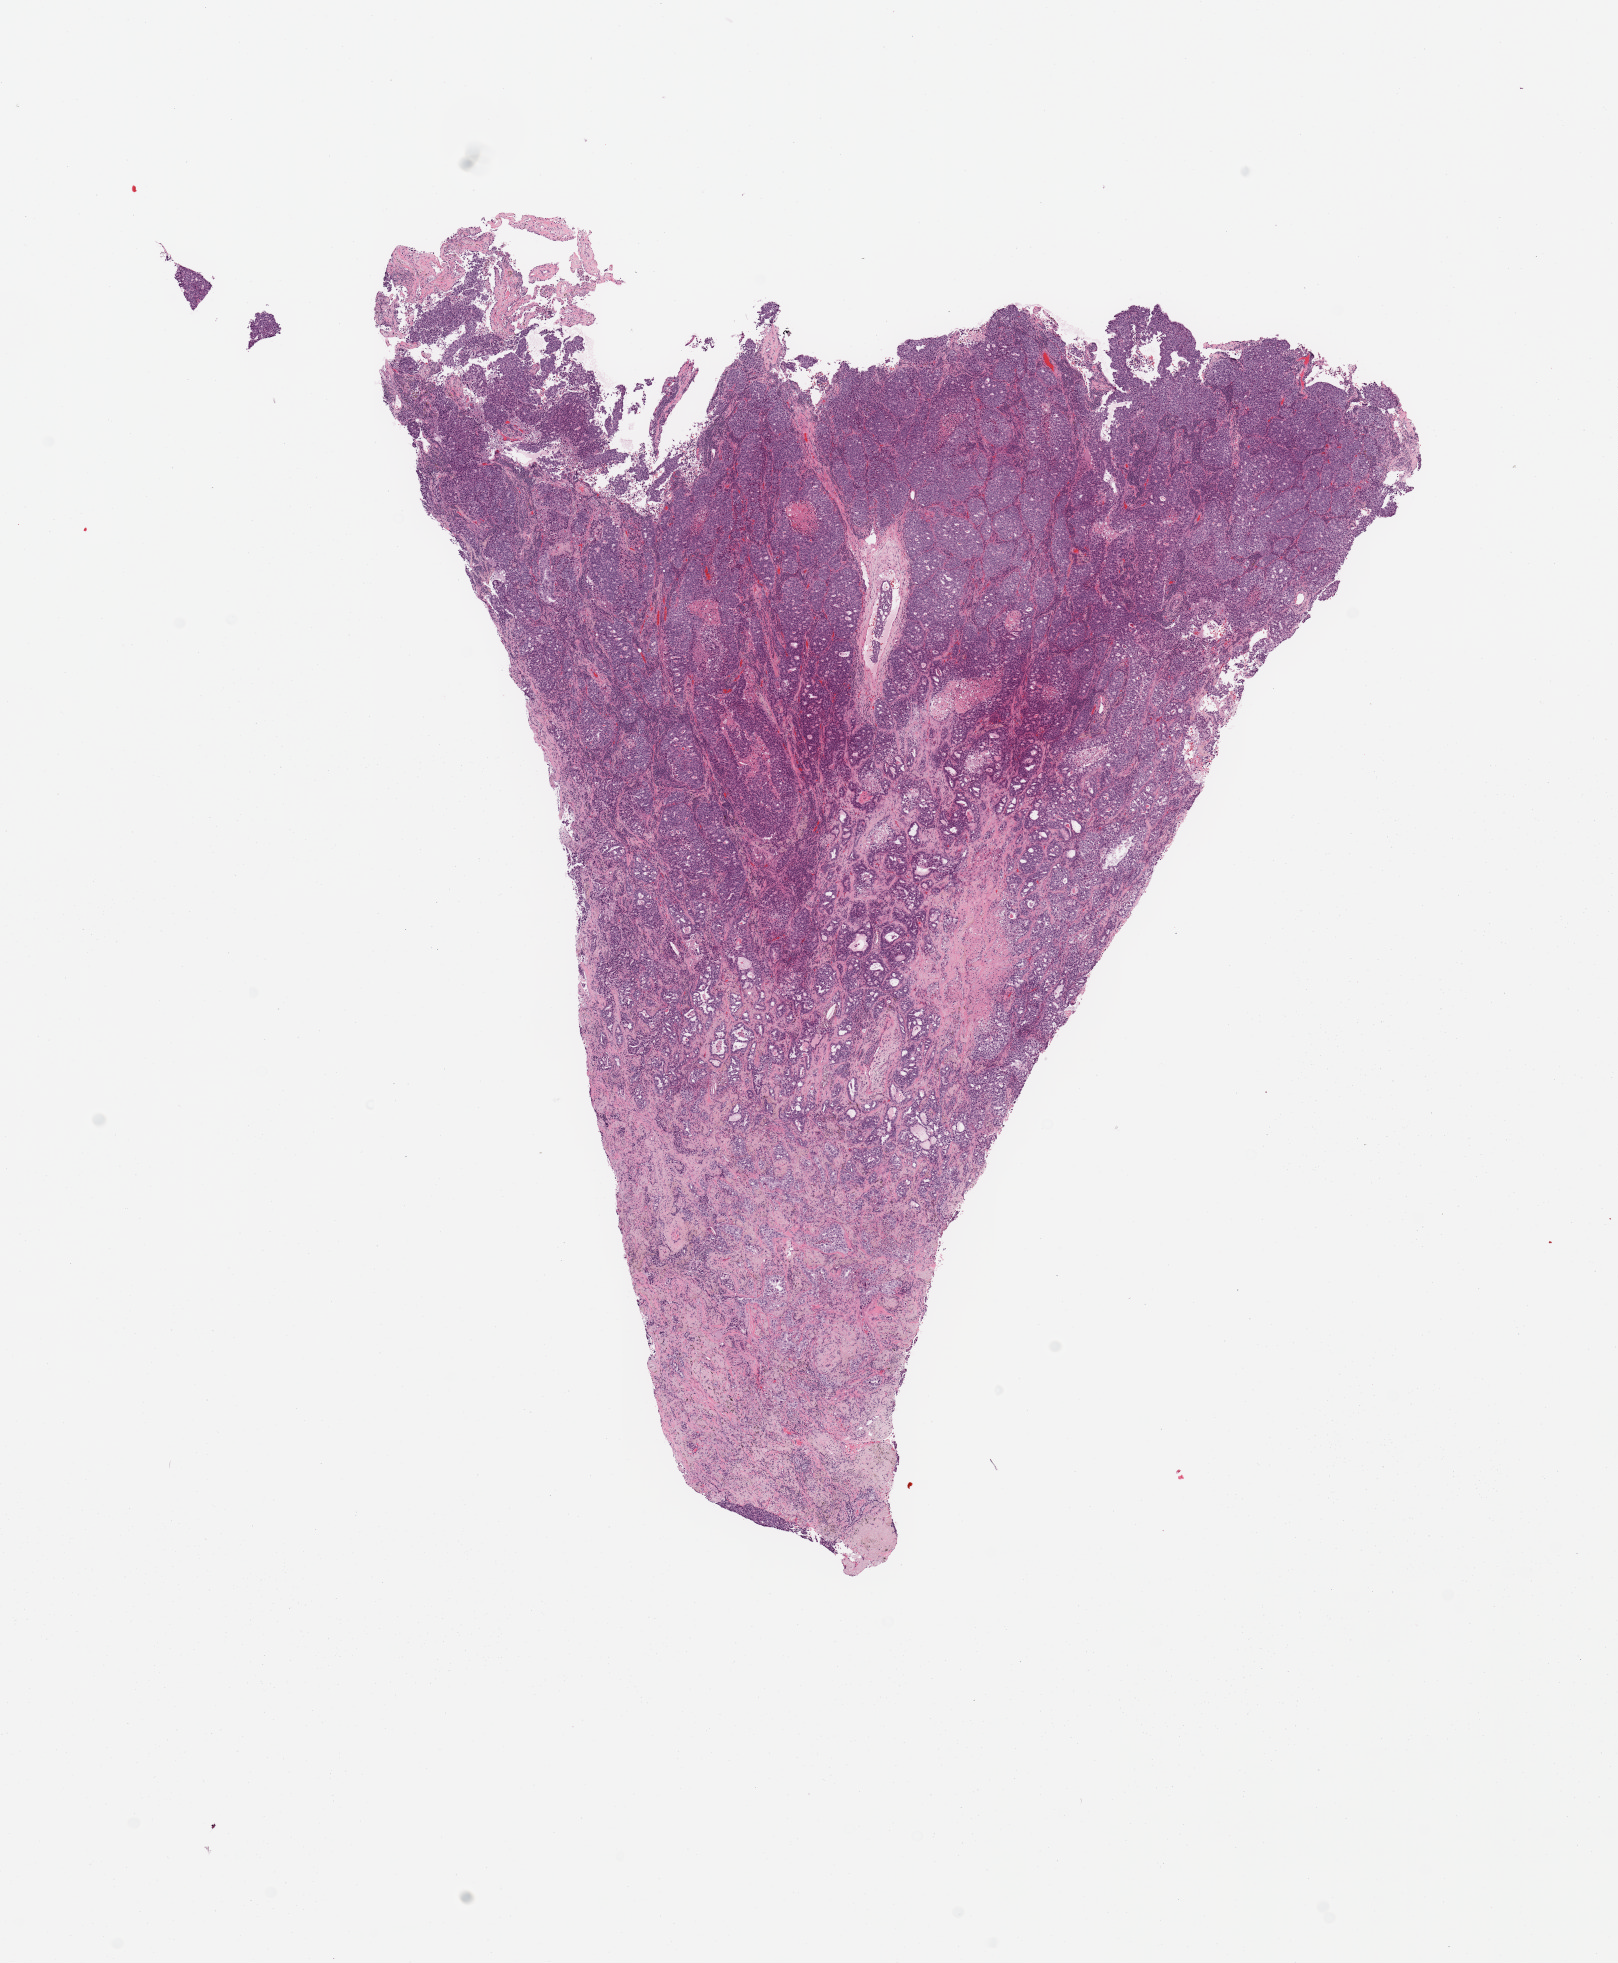
Hematoxylin and eosin (H&E) stained whole-slide image, low-resolution overview of the scanned area, about 12.8 x 15.5 mm (acquisition: 20x scan). Tumour tissue sample, sampled site: lung. Patient: male, age 58 years. Histologic grade: G2 (moderately differentiated). Composition of this section per pathologist review: tumour nuclei 65%, necrosis 5%.
Primary tumour site (as recorded): left lower lobe. AJCC pathologic stage: IB. Diagnosis: Adenocarcinoma, NOS.